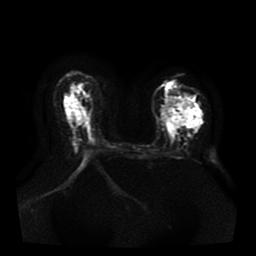
Breast MRI, one axial slice. Slice 26 of 41 in the series (ordered by position). Diffusion-weighted series; image 2 of 4 stored at this slice position (different b-values; order by instance number). 1.5 T. 5 mm slice thickness. 256 × 256 image matrix, field of view 330 × 330 mm. Female patient.
Outlined on this slice (outlined manually by an expert reader):
- tumour on diffusion-weighted imaging: bounding box (x1, y1, x2, y2) in pixels: (163, 98, 199, 137)